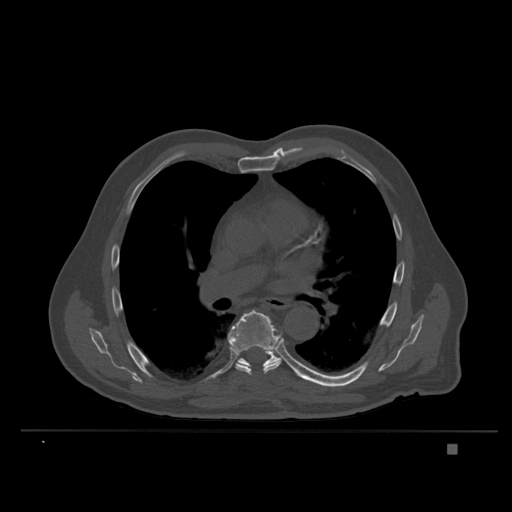
CT including the spine, one axial slice. Position 240 of 435 along the scan axis. Bone window (W 1800 / L 400 HU). 1.5 mm slice thickness. 512 × 512 image matrix, field of view 434 × 434 mm. Male patient, age 73 years. Case-level facts recorded for this patient, not image findings: primary cancer: skin.
Outlined on this slice (semi-automatically segmented with operator editing):
- T7 vertebra: bounding box (x1, y1, x2, y2) in pixels: (228, 309, 282, 376)
- T8 vertebra: (237, 351, 300, 376)